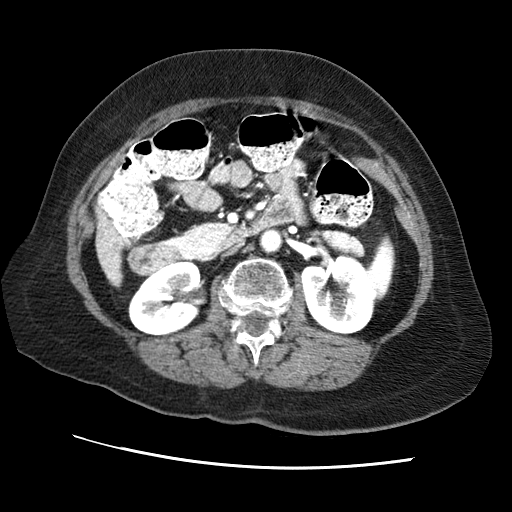
Contrast-enhanced abdominal CT (liver protocol), one axial slice; reconstruction kernel STANDARD; 120 kVp; soft-tissue window (W 400 / L 40 HU); 2.5 mm slice thickness; 512 × 512 image matrix, field of view 340 × 340 mm. Case-level facts recorded for this patient, not image findings: diagnosis: hepatocellular carcinoma (patient treated with transarterial chemoembolisation; whether this scan precedes or follows treatment is not stated here); TNM stage (as recorded): Stage-II; Child-Pugh class: A; tumour differentiation: no biopsy; tumour nodularity: multinodular.
Outlined on this slice (semi-automatic segmentation, software-assisted and operator-edited):
- liver parenchyma outside the tumour (the mass and vessels are separate outlines, so this box may not span the whole liver): bounding box [x1, y1, x2, y2] px = [96, 212, 124, 286]
- liver vessels: [104, 224, 121, 276]